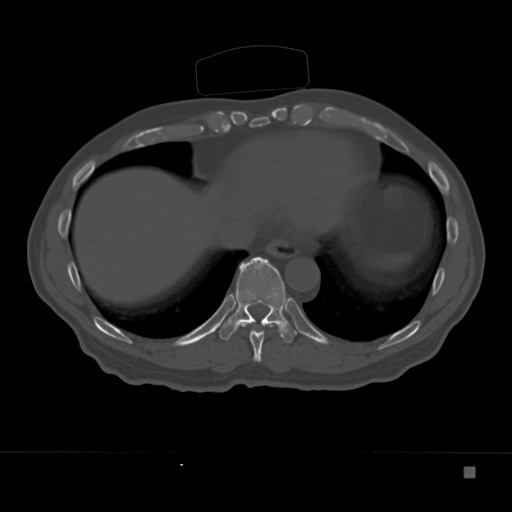
CT including the spine, one axial slice. Position 179 of 332 along the scan axis. Reconstruction kernel Br40s. Bone window (W 1800 / L 400 HU). 1.5 mm slice thickness. 512 × 512 image matrix. Patient: male, 72 years. Case-level facts recorded for this patient, not image findings: primary cancer: skeletal.
Outlined on this slice (semi-automatically segmented with operator editing):
- T10 vertebra: box from (x=219, y=257) to (x=297, y=343) px
- T9 vertebra: (x=236, y=322)–(x=280, y=362)